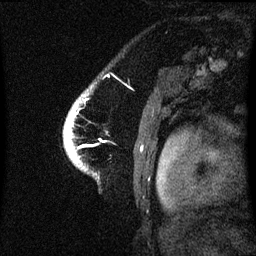
Breast MRI (dynamic contrast-enhanced), one sagittal slice; slice 55 of 60 in the series (ordered by position); dynamic contrast-enhanced series, image 2 of 3 at this slice position (ordered by acquisition); 1.5 T; TE 4.2 ms, TR 8.4 ms; 256 × 256 image matrix, field of view 220 × 220 mm. Female patient, age 53 years. Case-level facts recorded for this patient, not image findings: setting: breast cancer imaged before/during neoadjuvant chemotherapy; receptor status: HR-positive, HER2-negative.
Annotated regions visible in this slice (semi-automatic segmentation, software-assisted and operator-edited):
- analysis volume of interest (the breast-tissue region the enhancement analysis was run in; not a lesion): bounding box (x1, y1, x2, y2) in pixels: (65, 112, 80, 163)
- tumour enhancement mask (voxels above the 70 % enhancement threshold inside the analysis volume of interest): (66, 132, 71, 151)